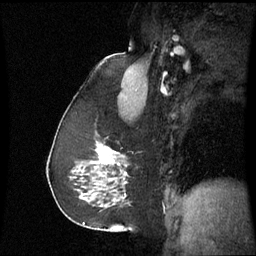
Breast MRI (dynamic contrast-enhanced), one sagittal slice; position 38 of 60 along the scan axis; dynamic contrast-enhanced series, image 2 of 3 at this slice position (ordered by acquisition); 1.5 T; TE 4.2 ms, TR 8.9 ms; 2.4 mm slice thickness; 256 × 256 image matrix, field of view 220 × 220 mm. Female patient, age 59 years. Case-level facts recorded for this patient, not image findings: setting: breast cancer imaged before/during neoadjuvant chemotherapy; receptor status: triple-negative.
Structures marked on this image (semi-automatically segmented with operator editing):
- analysis volume of interest (the breast-tissue region the enhancement analysis was run in; not a lesion): bounding box (x1, y1, x2, y2) in pixels: (88, 132, 129, 197)
- tumour enhancement mask (voxels above the 70 % enhancement threshold inside the analysis volume of interest): (100, 148, 115, 165)